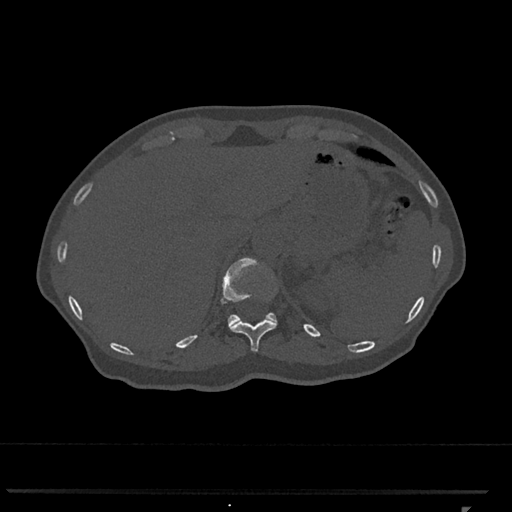
CT including the spine, one axial slice; slice 498 of 793 in the series (ordered by position); reconstruction kernel Br40s/3; bone window (W 1800 / L 400 HU); 0.5 mm slice thickness; 512 × 512 image matrix, field of view 380 × 380 mm. Female patient, age 62 years. Case-level facts recorded for this patient, not image findings: primary cancer: renal.
Structures marked on this image (semi-automatically segmented with operator editing):
- T11 vertebra: bounding box [x1, y1, x2, y2] px = [228, 319, 277, 352]
- T12 vertebra: [220, 257, 277, 326]